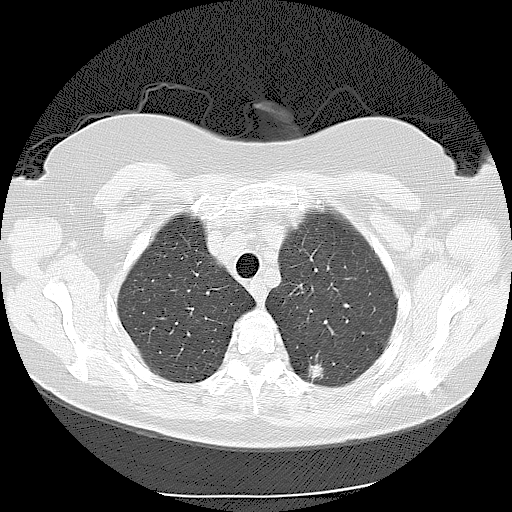
Chest CT (low-dose screening protocol), one axial image; second annual screen; lung window (W 1500 / L -600 HU); 2.5 mm slice thickness; slice 25 of 116 in the series. Female, age 56 years at enrolment.
- Expert-annotated lung lesion, bounding box [x1, y1, x2, y2] px = [290, 346, 344, 394].
- Reader record for this screening exam (exam-level; its link to the box is not recorded): non-calcified nodule or mass ≥4 mm, left lower lobe, 9 × 9 mm, spiculated (stellate) margins, soft tissue attenuation, pre-existing on the prior screen: yes; interval growth: yes.
- Participant outcome: lung cancer diagnosed 173 days after this screen — adenocarcinoma, NOS, left lower lobe, moderately differentiated (G2), stage IIA (AJCC 6th edition), 15 mm at pathology.